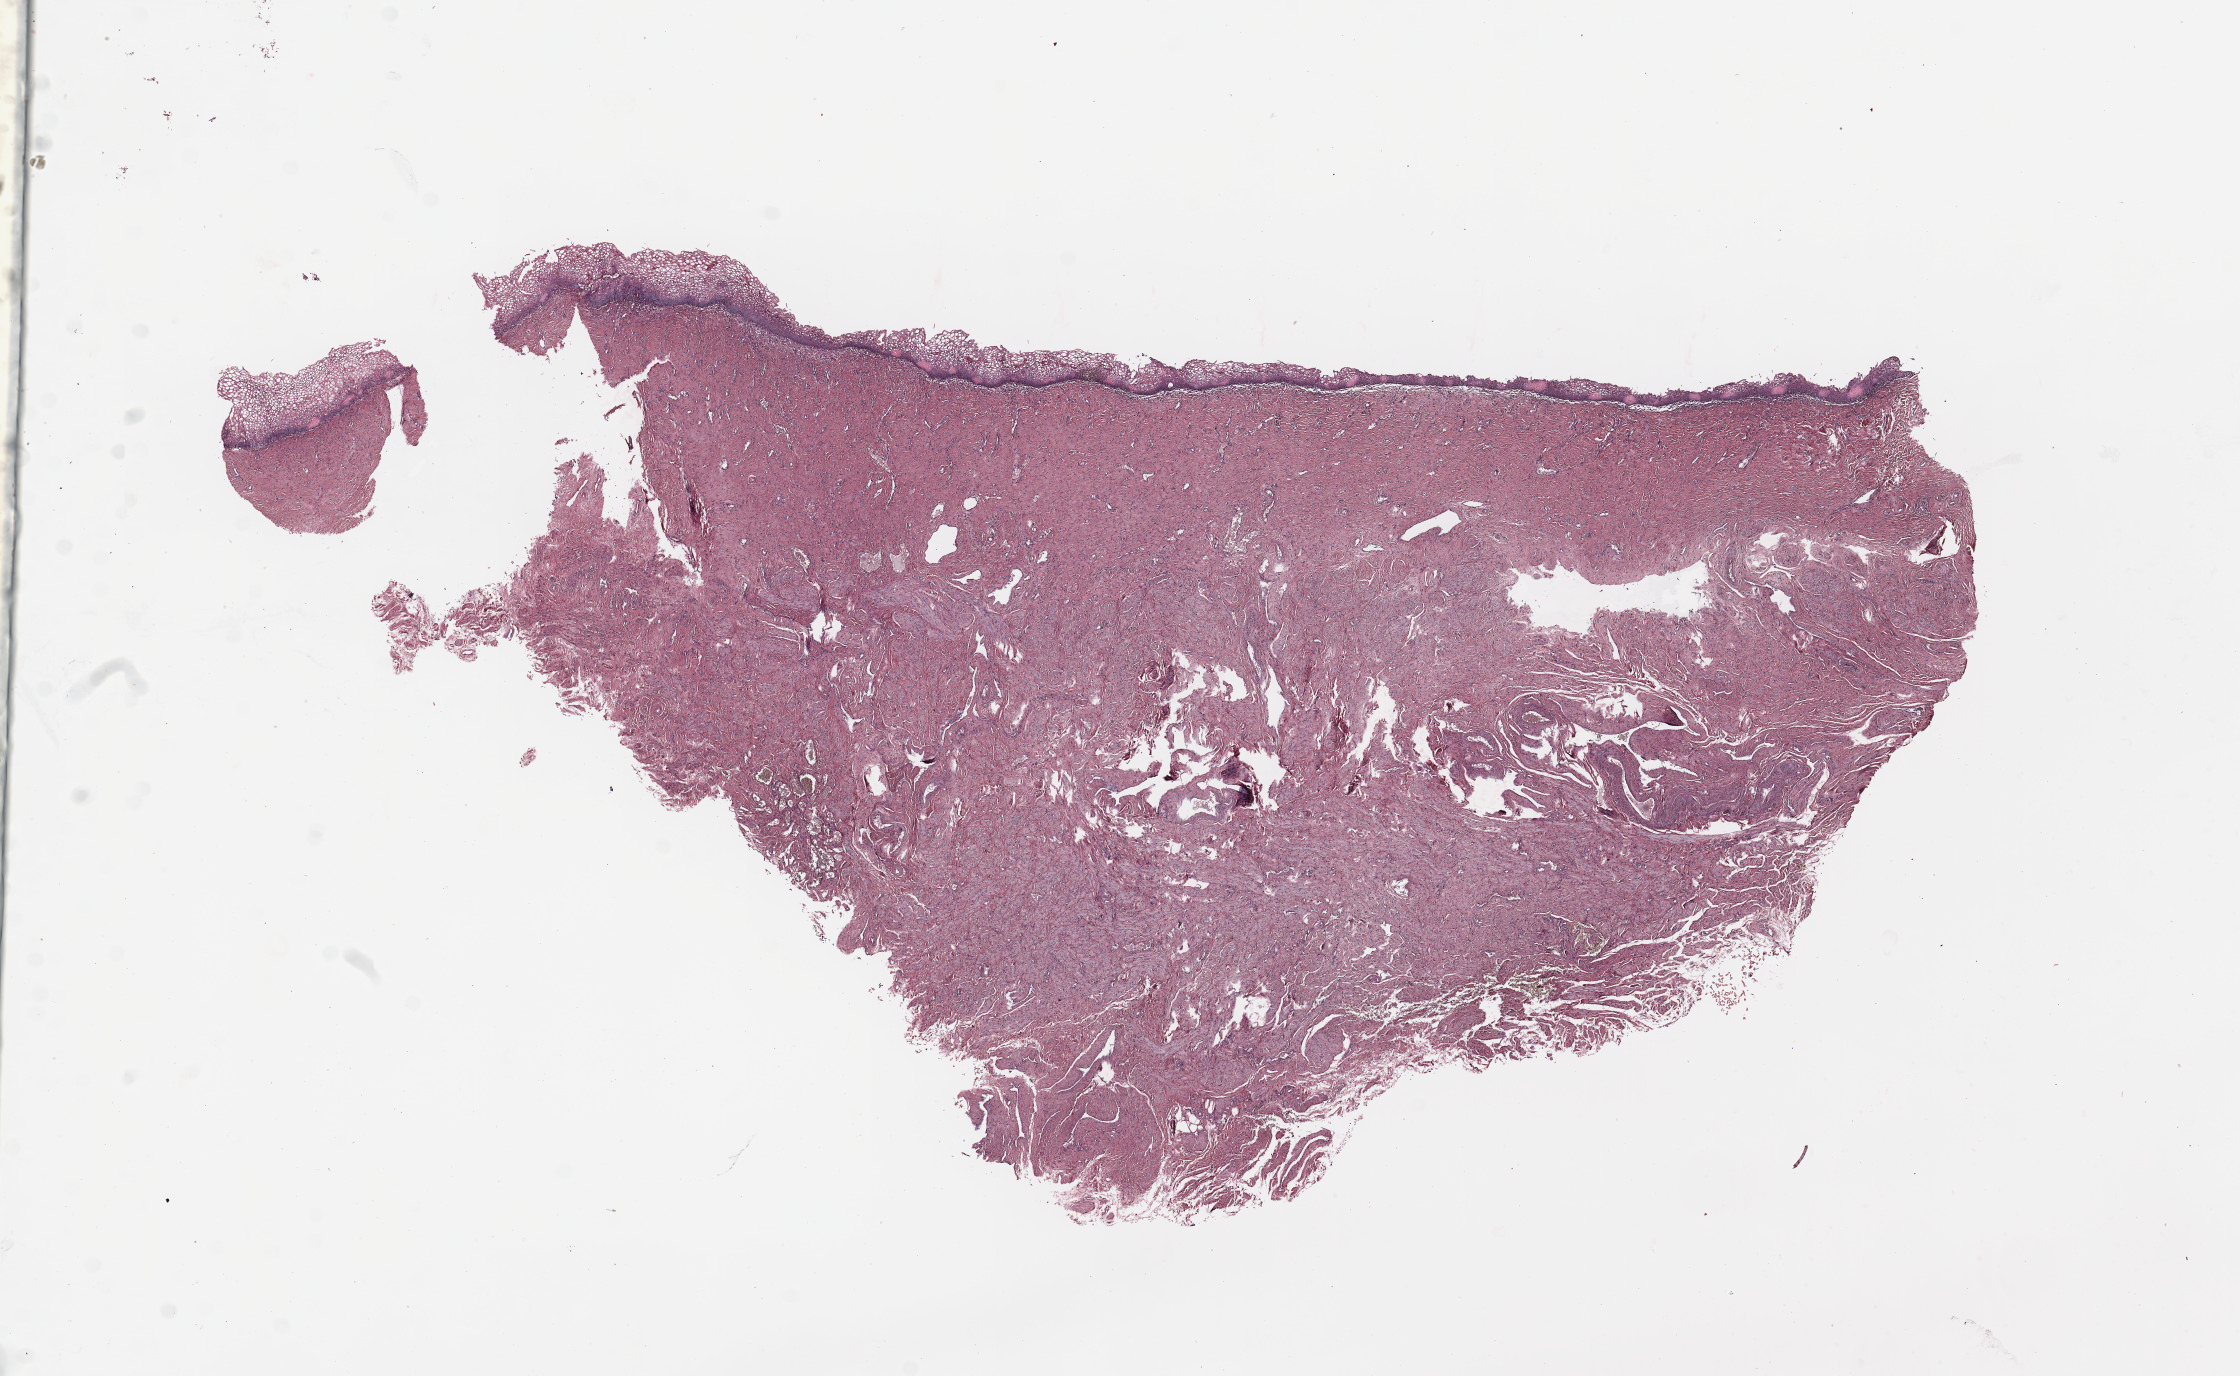
Digitized H&E tissue section (whole slide) — whole scanned area (about 17.7 x 10.9 mm, slide scanned at 20x) shown as a low-resolution overview. Uterus, normal (non-tumour) tissue. Female, 69 y/o.
- this section: normal (non-tumour) tissue from the same patient
- patient diagnosis: Endometrioid adenocarcinoma, NOS